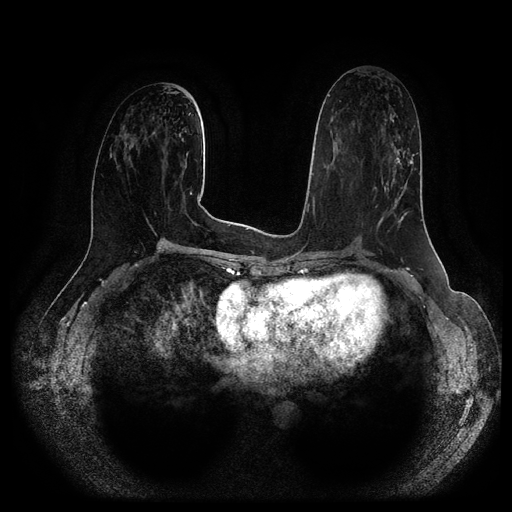
Breast MRI (dynamic contrast-enhanced, multi-phase), one axial slice. Position 51 of 116 along the scan axis. Dynamic contrast-enhanced series, time point 2 of 5 at this slice position (early post-contrast). 1.5 T. TE 2.6 ms, TR 5.2 ms. 2 mm slice thickness. 512 × 512 image matrix. Patient: female, 57 years.
Outlined on this slice (semi-automatic segmentation, software-assisted and operator-edited):
- breast lesion (labelled 'tumour' in the annotation; benign lesions carry a separate 'benign' label): bounding box [x1, y1, x2, y2] px = [381, 138, 415, 209]